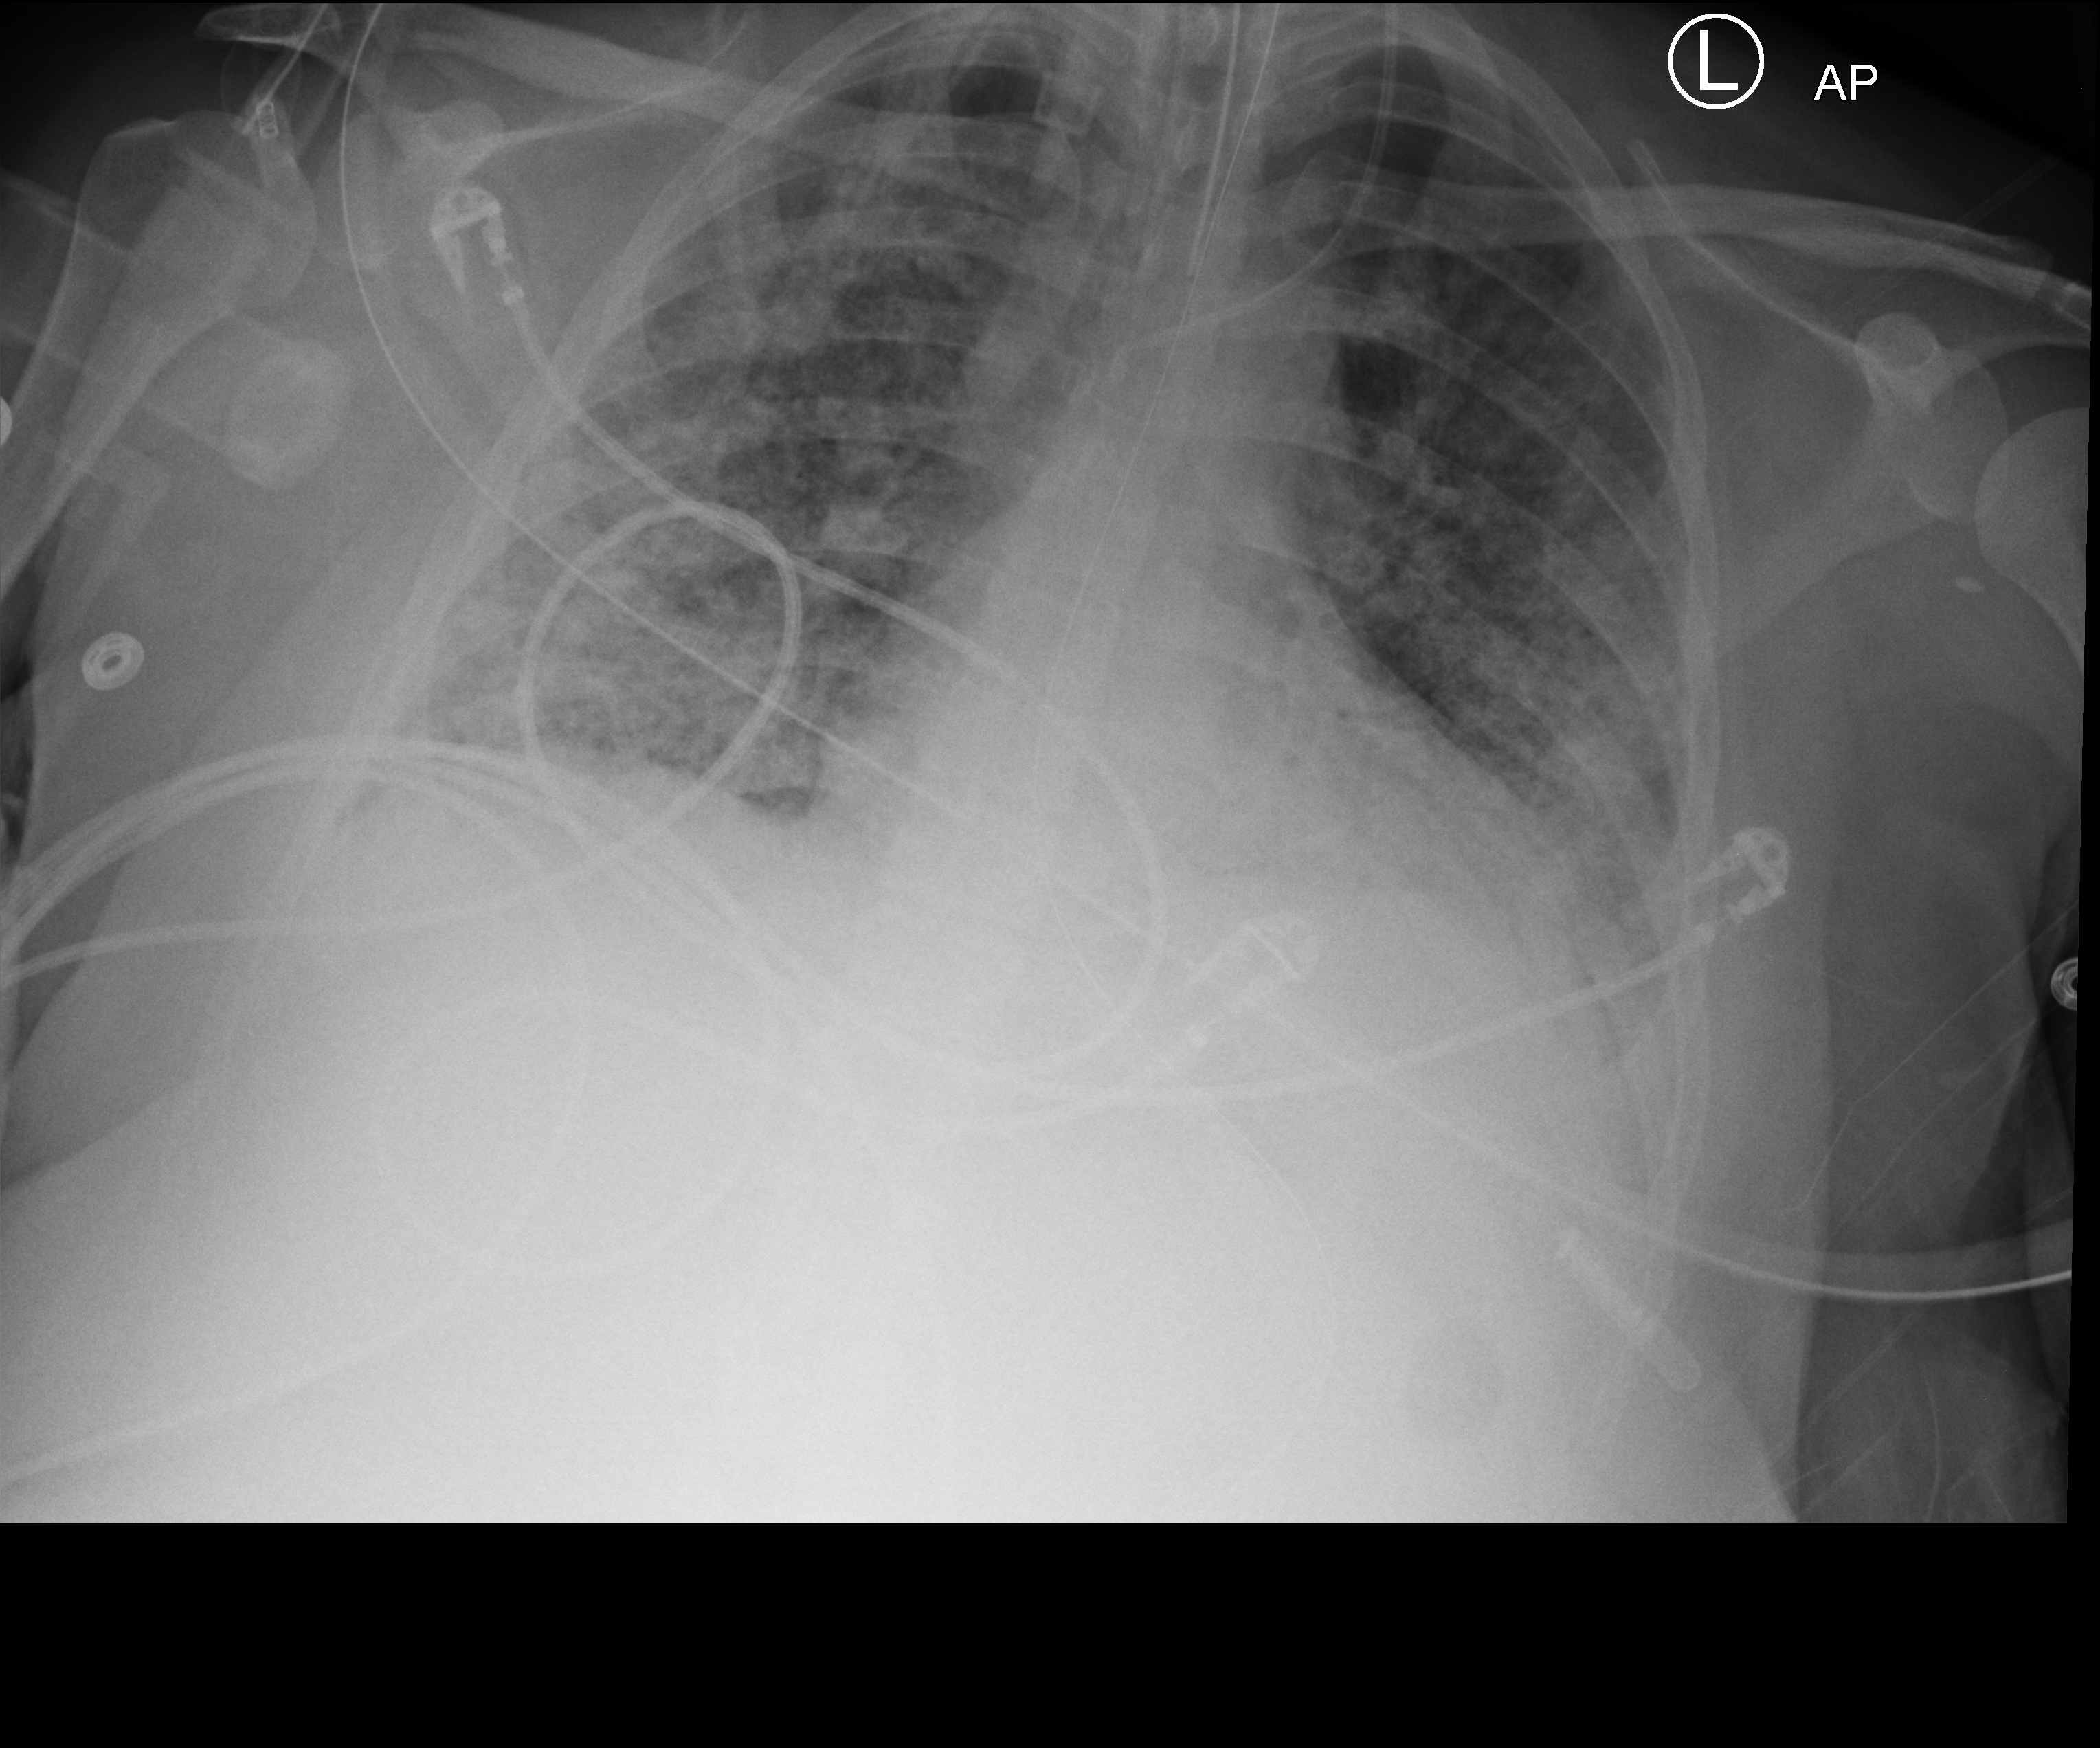
Portable chest radiograph, anteroposterior (AP) projection. Patient hospitalised with COVID-19; female, aged 18–59 years.
From the hospital-stay record, not from the radiograph (when in the stay this image was taken is not recorded):
- mechanically ventilated during this hospital stay: yes